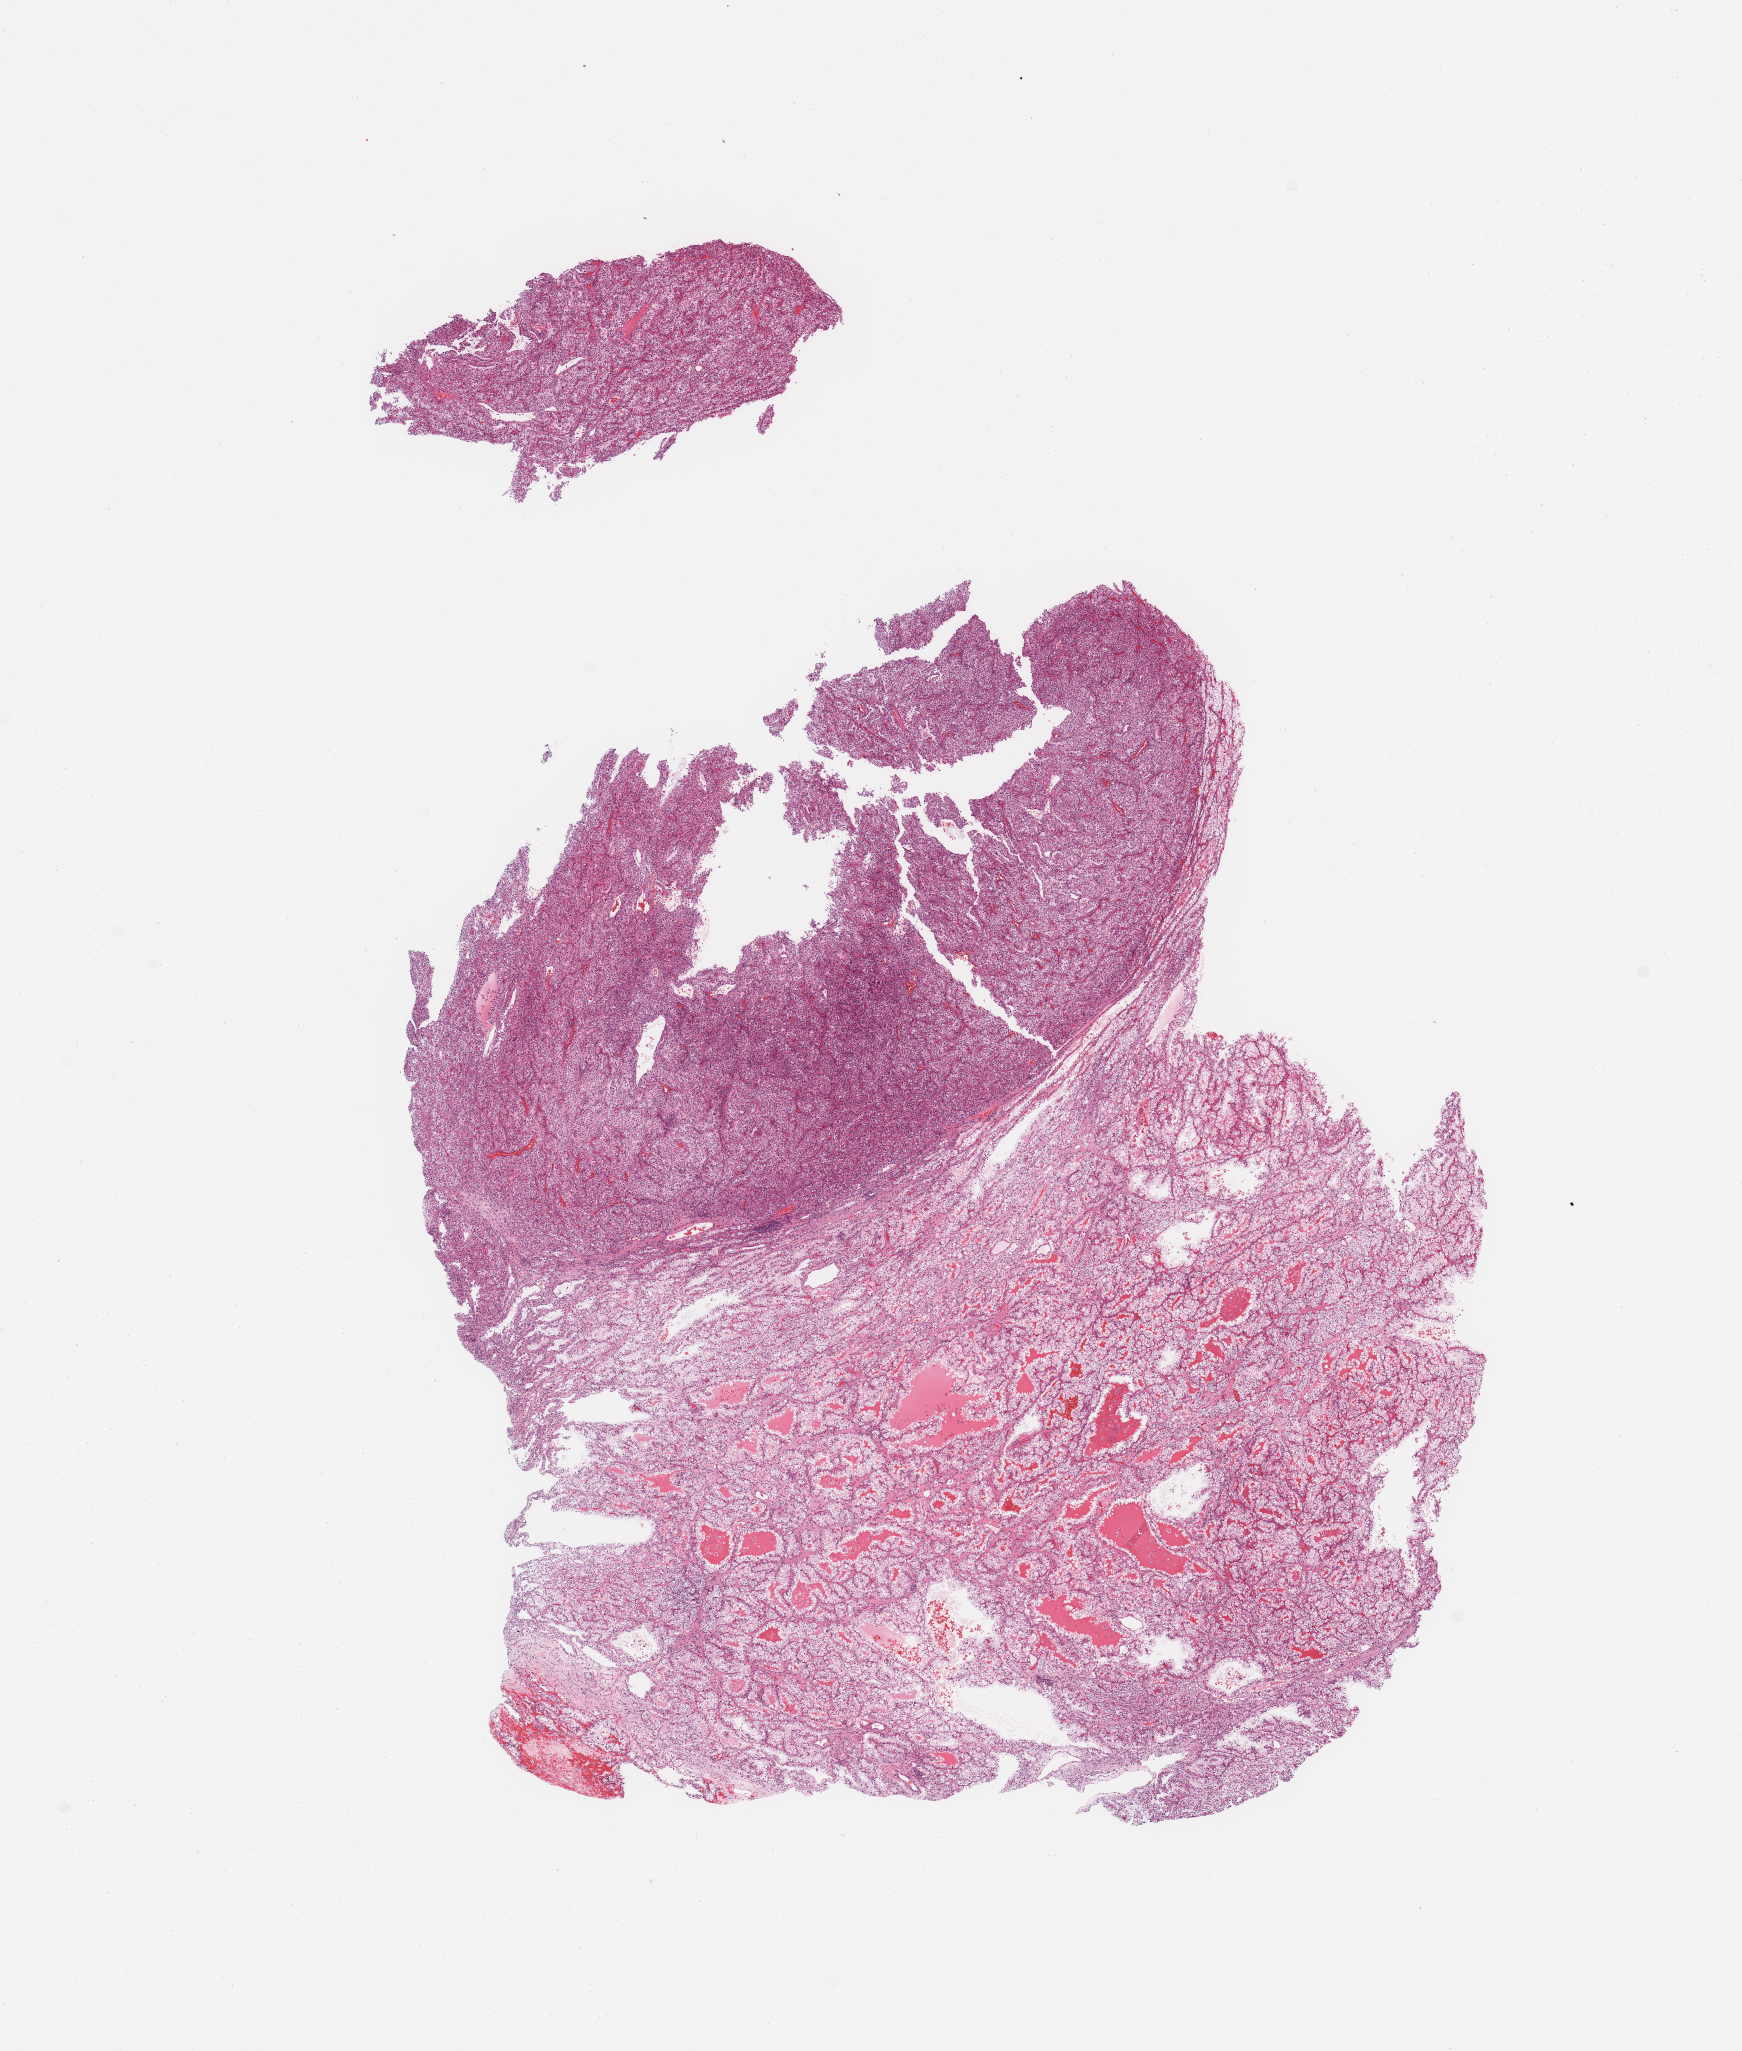
Digitized Hematoxylin and eosin (H&E) stained tissue section (whole slide), whole scanned area (about 13.8 x 16.2 mm, slide scanned at 20x) shown as a low-resolution overview; tumour tissue sample, sampled site: kidney. Male, 55 y/o. Histologic grade: G3 (poorly differentiated). Pathologist review of this section (percent, as recorded): tumour nuclei 90%, necrosis 0%.
Histologic diagnosis: Renal cell carcinoma, NOS. AJCC pathologic stage: I.